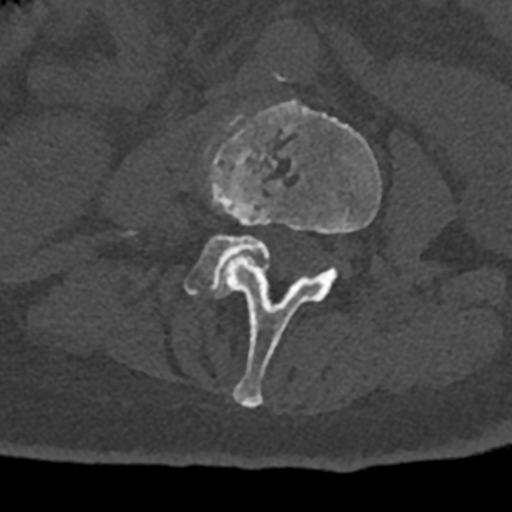
CT including the spine, one axial slice; slice 301 of 797 in the series (ordered by position); 120 kVp; bone window (W 1800 / L 400 HU); 0.5 mm slice thickness; 512 × 512 image matrix, field of view 160 × 160 mm. Male patient, age 74 years. From the clinical record (not read from this slice): primary cancer: renal; vertebrae with lytic lesions (as recorded): T10, L1, L2, L3, L4, L5.
Annotated regions visible in this slice (semi-automatic segmentation, software-assisted and operator-edited):
- L3 vertebra: bounding box <206,101,382,408> (left, top, right, bottom; pixels)
- L4 vertebra: <184,235,338,298>